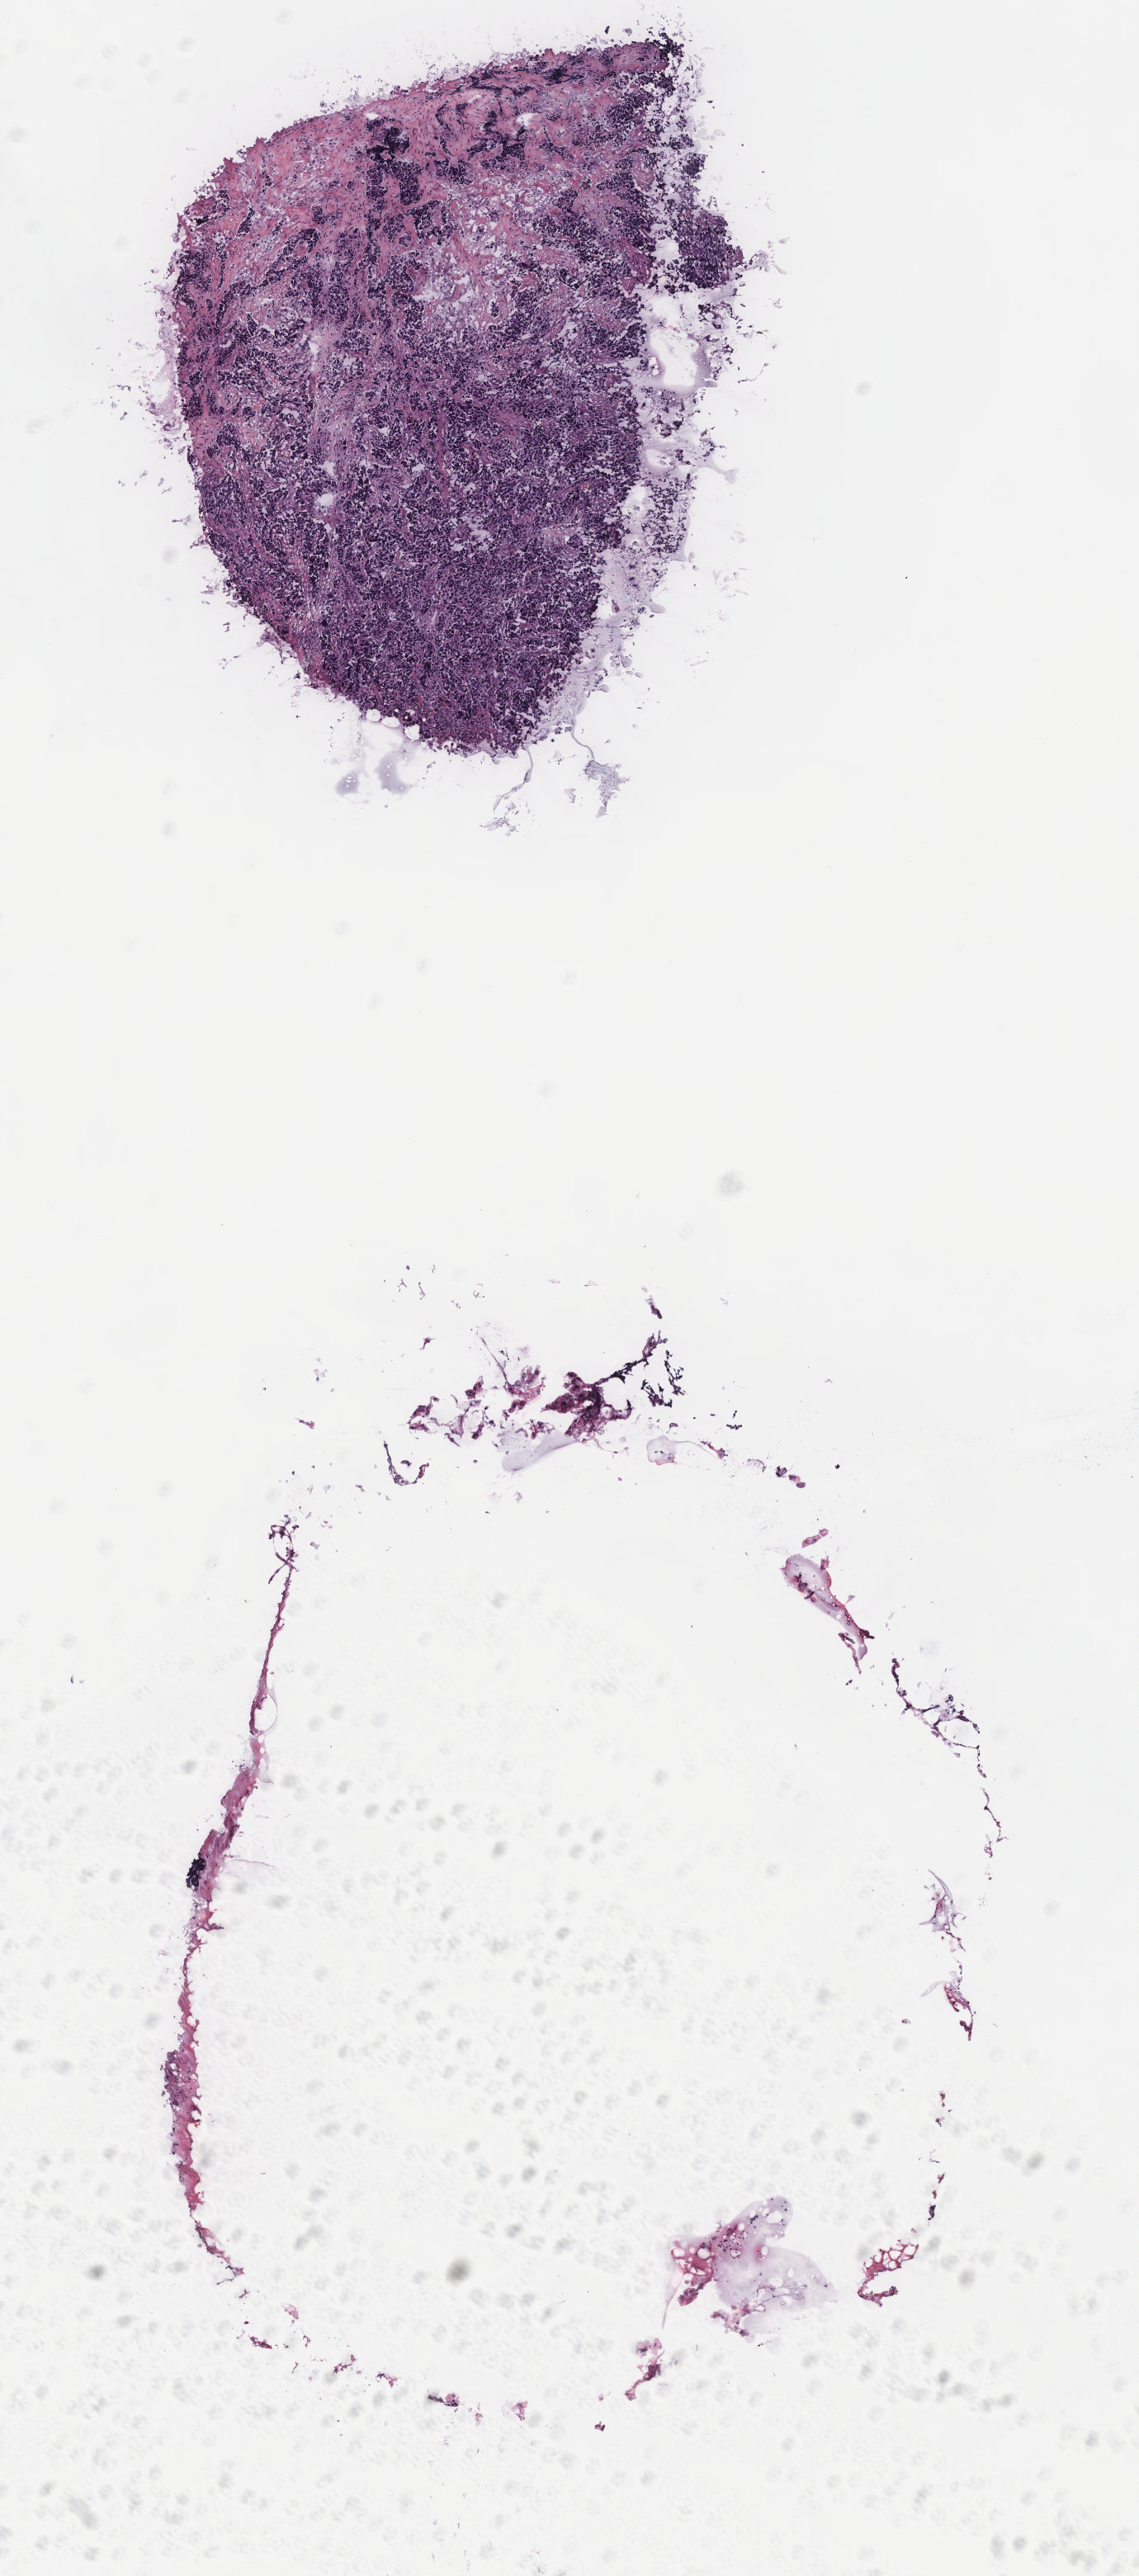
Digitized H&E-stained tissue section (whole slide) — low-resolution overview of the scanned area, about 5.5 x 12.5 mm. Female, 45 y/o.
* specimen: breast, tumour tissue